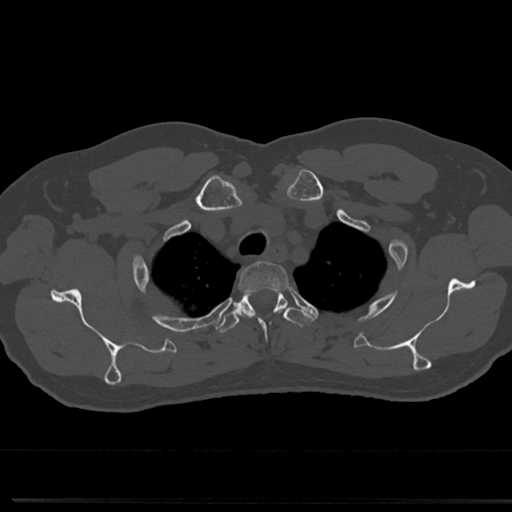
CT including the spine, one axial slice. Position 611 of 817 along the scan axis. Reconstruction kernel Br40s/3. 120 kVp. Bone window (W 1800 / L 400 HU). 512 × 512 image matrix, field of view 355 × 355 mm. Patient: male, 61 years. From the clinical record (not read from this slice): primary cancer: prostate.
Annotated regions visible in this slice (semi-automatic segmentation, software-assisted and operator-edited):
- T2 vertebra: bounding box [x1, y1, x2, y2] px = [239, 262, 289, 289]
- T3 vertebra: [215, 289, 311, 334]